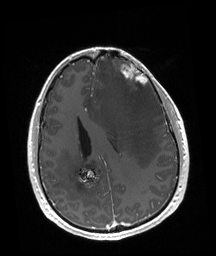
Brain MRI from a brain-tumour surgery series, one axial slice. Slice 69 of 192 in the series (ordered by position). T1-weighted post-contrast. 1 mm slice thickness. 216 × 256 image matrix. Case-level facts recorded for this patient, not image findings: tumour location: Left Frontal.
Structures marked on this image (outlined manually by an expert reader):
- tumour: bounding box [x1, y1, x2, y2] px = [121, 65, 147, 90]